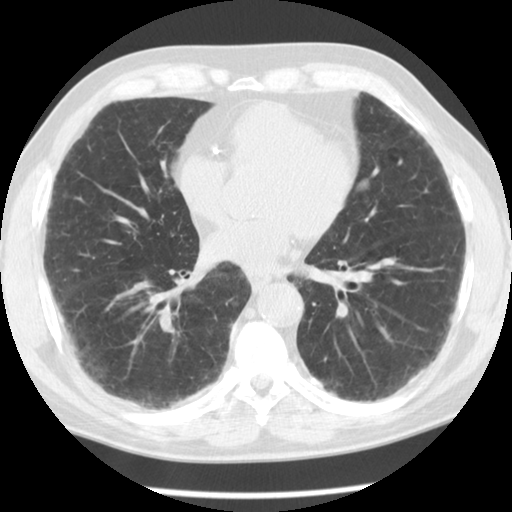
Low-dose screening chest CT, one axial slice. Slice 49 of 113 in the series (ordered by position). Reconstruction kernel STANDARD. 120 kVp. Lung window (W 1500 / L -600 HU). 2.5 mm slice thickness. 512 × 512 image matrix, field of view 330 × 330 mm.
Outlined on this slice (manually delineated by an expert):
- lesion 1 (nodule, upper lobe of left lung): bounding box <359,180,368,188> (left, top, right, bottom; pixels)